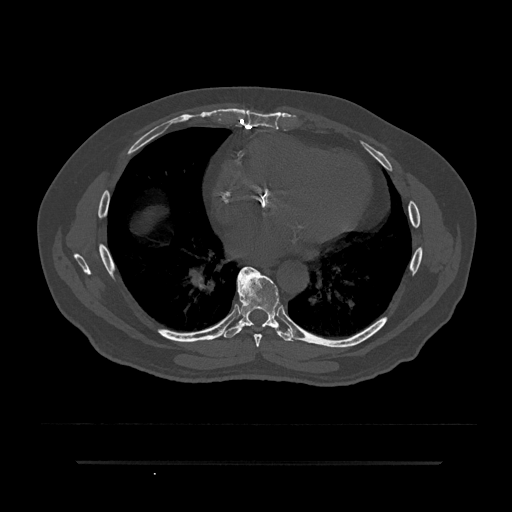
CT including the spine, one axial slice. Position 449 of 797 along the scan axis. 120 kVp. Bone window (W 1800 / L 400 HU). 0.5 mm slice thickness. 512 × 512 image matrix, field of view 464 × 464 mm. Patient: male, 59 years. Case-level facts recorded for this patient, not image findings: primary cancer: bile ducts; vertebrae with lytic lesions (as recorded): T10.
Outlined on this slice (semi-automatically segmented with operator editing):
- T7 vertebra: box from (x=237, y=266) to (x=268, y=347) px
- T8 vertebra: (x=222, y=269)–(x=295, y=342)